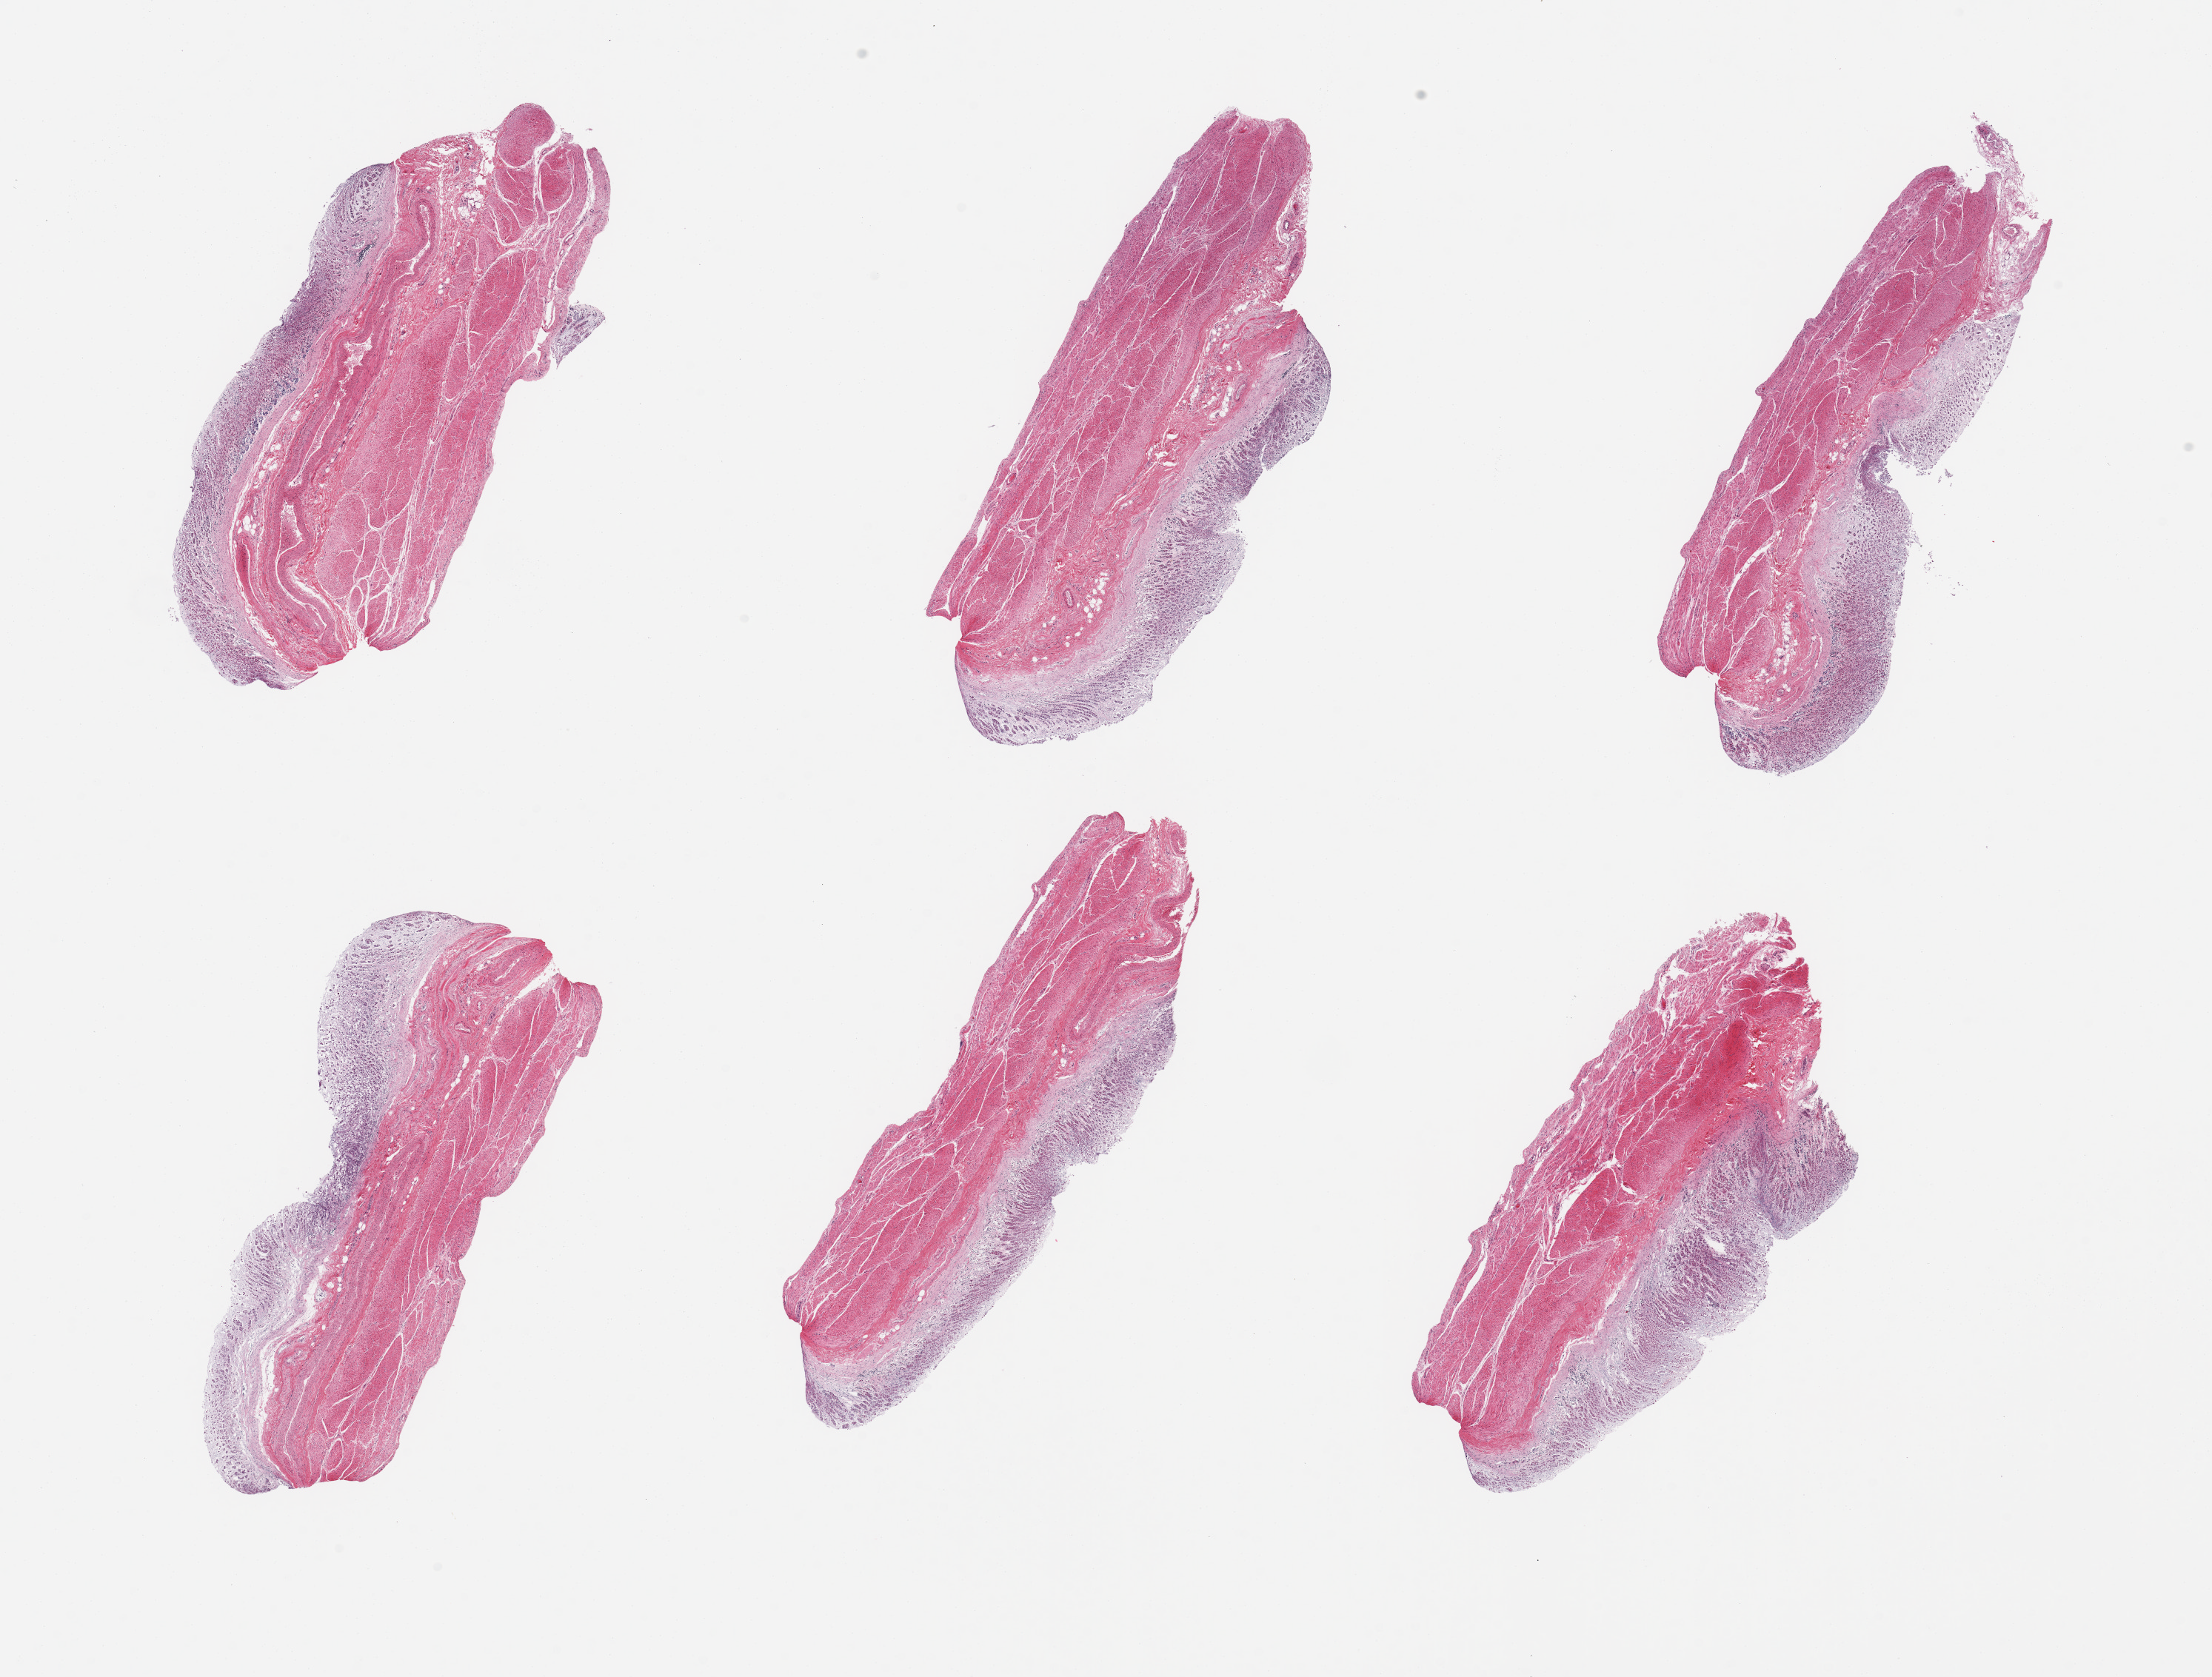
Hematoxylin and eosin (H&E) whole-slide image, low-resolution overview of the scanned area, about 23.6 x 17.9 mm, PAXgene-fixed, paraffin-embedded tissue, sampled site (target tissue): stomach, tissue donor sample. Donor: female.
Reviewer comment on this tissue sample: 6 pieces; fill thickness sections, mucosa largely autolyzed.